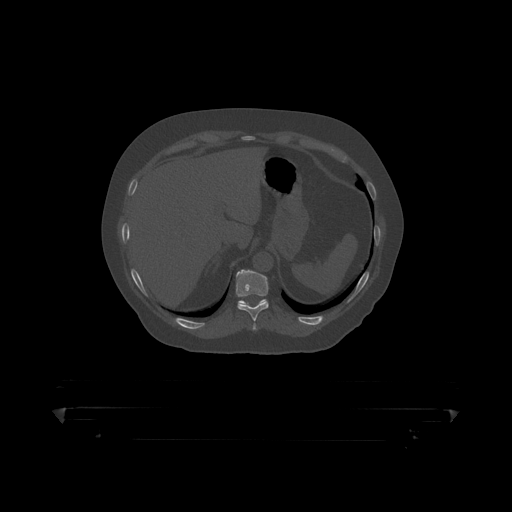
CT including the spine, one axial slice; slice 212 of 390 in the series (ordered by position); reconstruction kernel STANDARD; bone window (W 1800 / L 400 HU); 512 × 512 image matrix, field of view 650 × 650 mm. Male patient, age 60 years. Case-level facts recorded for this patient, not image findings: primary cancer: prostate.
Structures marked on this image (semi-automatic segmentation, software-assisted and operator-edited):
- T10 vertebra: bounding box (x1, y1, x2, y2) in pixels: (236, 270, 269, 319)
- T11 vertebra: (239, 299, 266, 305)